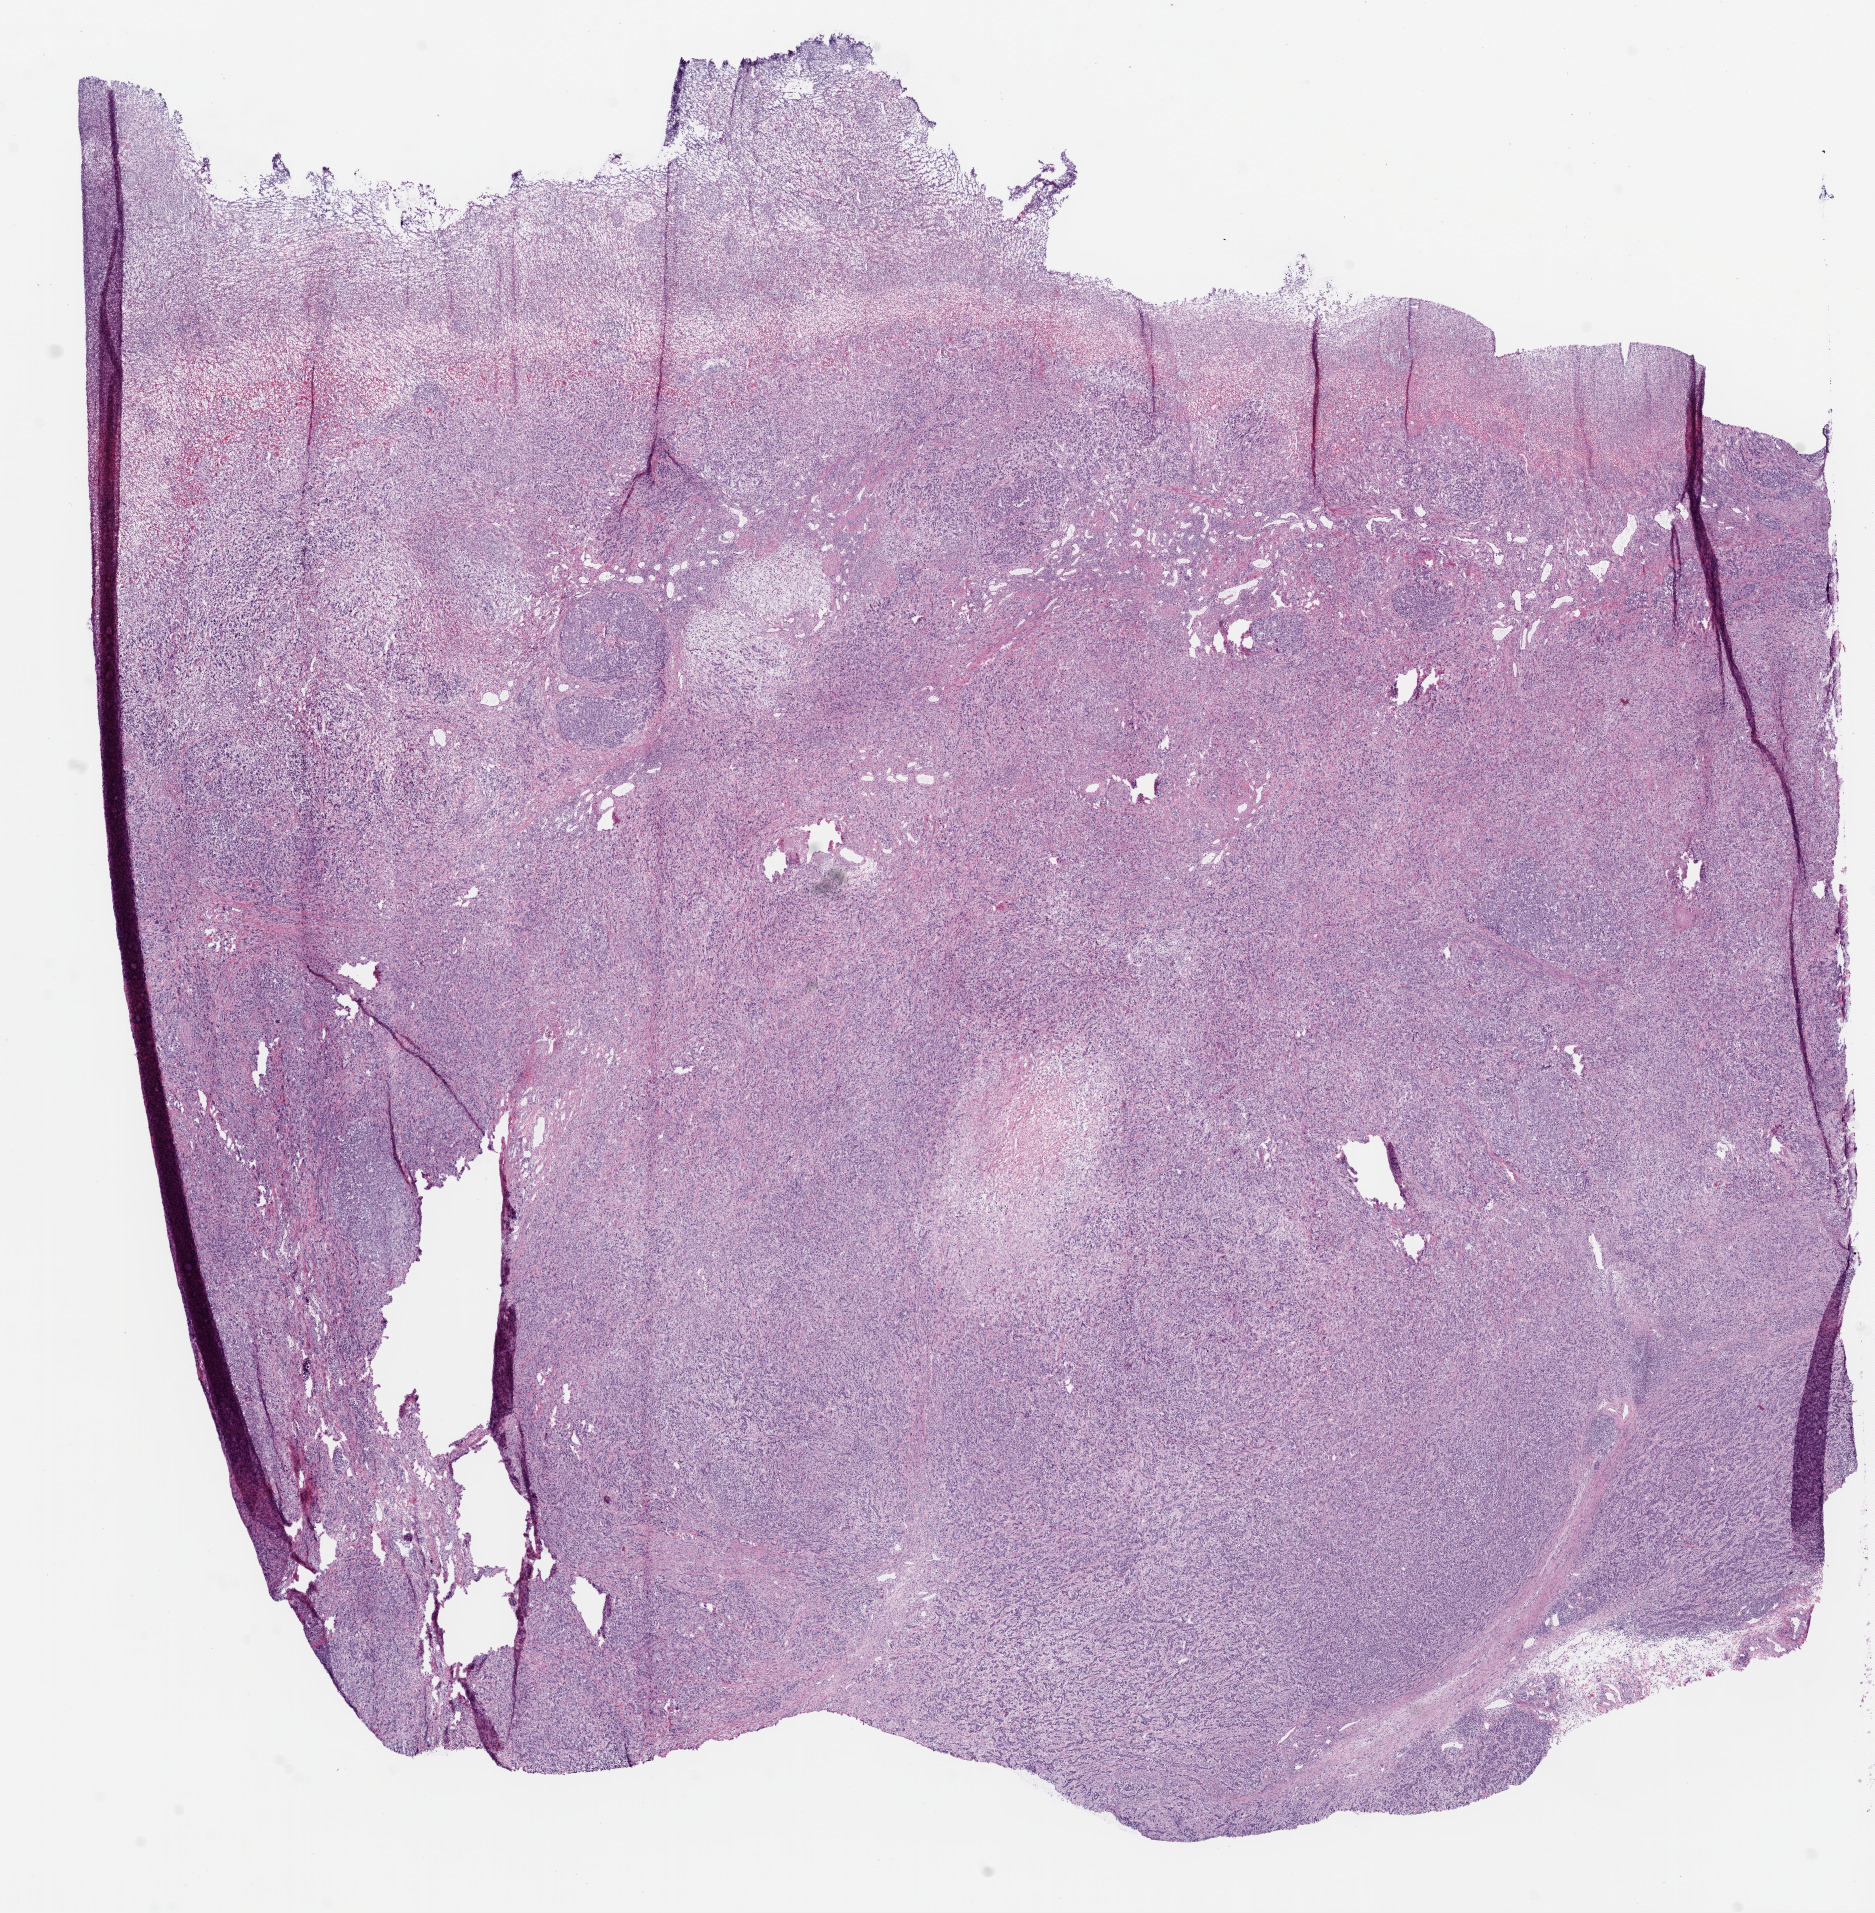
H&E-stained whole-slide image — shown as a low-resolution overview of the whole scanned area (about 15.0 x 15.4 mm), frozen section from the bottom of the tissue portion, primary tumour sample from the stomach. Male, age 78 years at initial diagnosis. Histologic grade: G3 (poorly differentiated). Composition of this section per pathologist review: tumour cells 90%, tumour nuclei 75%, normal cells 0%, stromal cells 5%, necrosis 5%.
Pathologic diagnosis: Adenocarcinoma, NOS (gastric antrum).